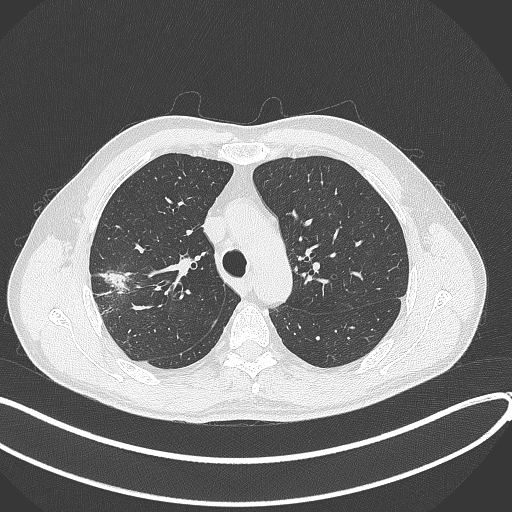
Chest CT, one axial slice. Slice 303 of 381 in the series (ordered by position). Reconstruction kernel B70f. Lung window (W 1500 / L -600 HU). 1 mm slice thickness. 512 × 512 image matrix. Male patient, age 62 years. From the clinical record (not read from this slice): clinical TNM (as recorded): T1c N0 M0; histopathological grade: G2-3.
Annotated regions visible in this slice (rectangle marked by the reading radiologist):
- lung tumour (recorded histology: adenocarcinoma): box from (x=101, y=268) to (x=130, y=293) px